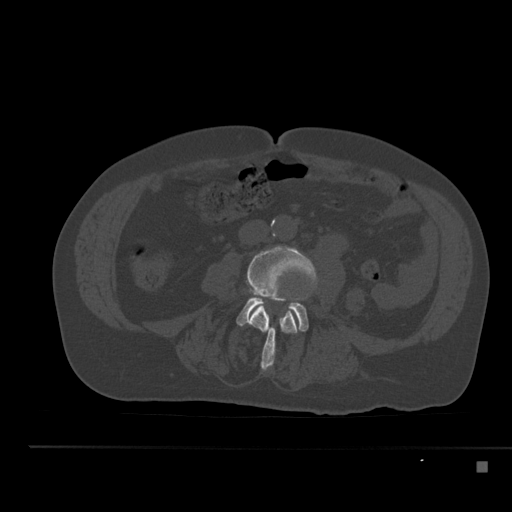
CT including the spine, one axial slice; slice 154 of 517 in the series (ordered by position); reconstruction kernel Br40s; bone window (W 1800 / L 400 HU); 1.5 mm slice thickness; 512 × 512 image matrix, field of view 408 × 408 mm. Male patient, age 70 years. Case-level facts recorded for this patient, not image findings: primary cancer: renal; vertebrae with lytic lesions (as recorded): T4, T6, T10, T12, L3, L4, L5.
Structures marked on this image (semi-automatic segmentation, software-assisted and operator-edited):
- L3 vertebra: bounding box (x1, y1, x2, y2) in pixels: (247, 247, 318, 371)
- L4 vertebra: (237, 296, 309, 331)